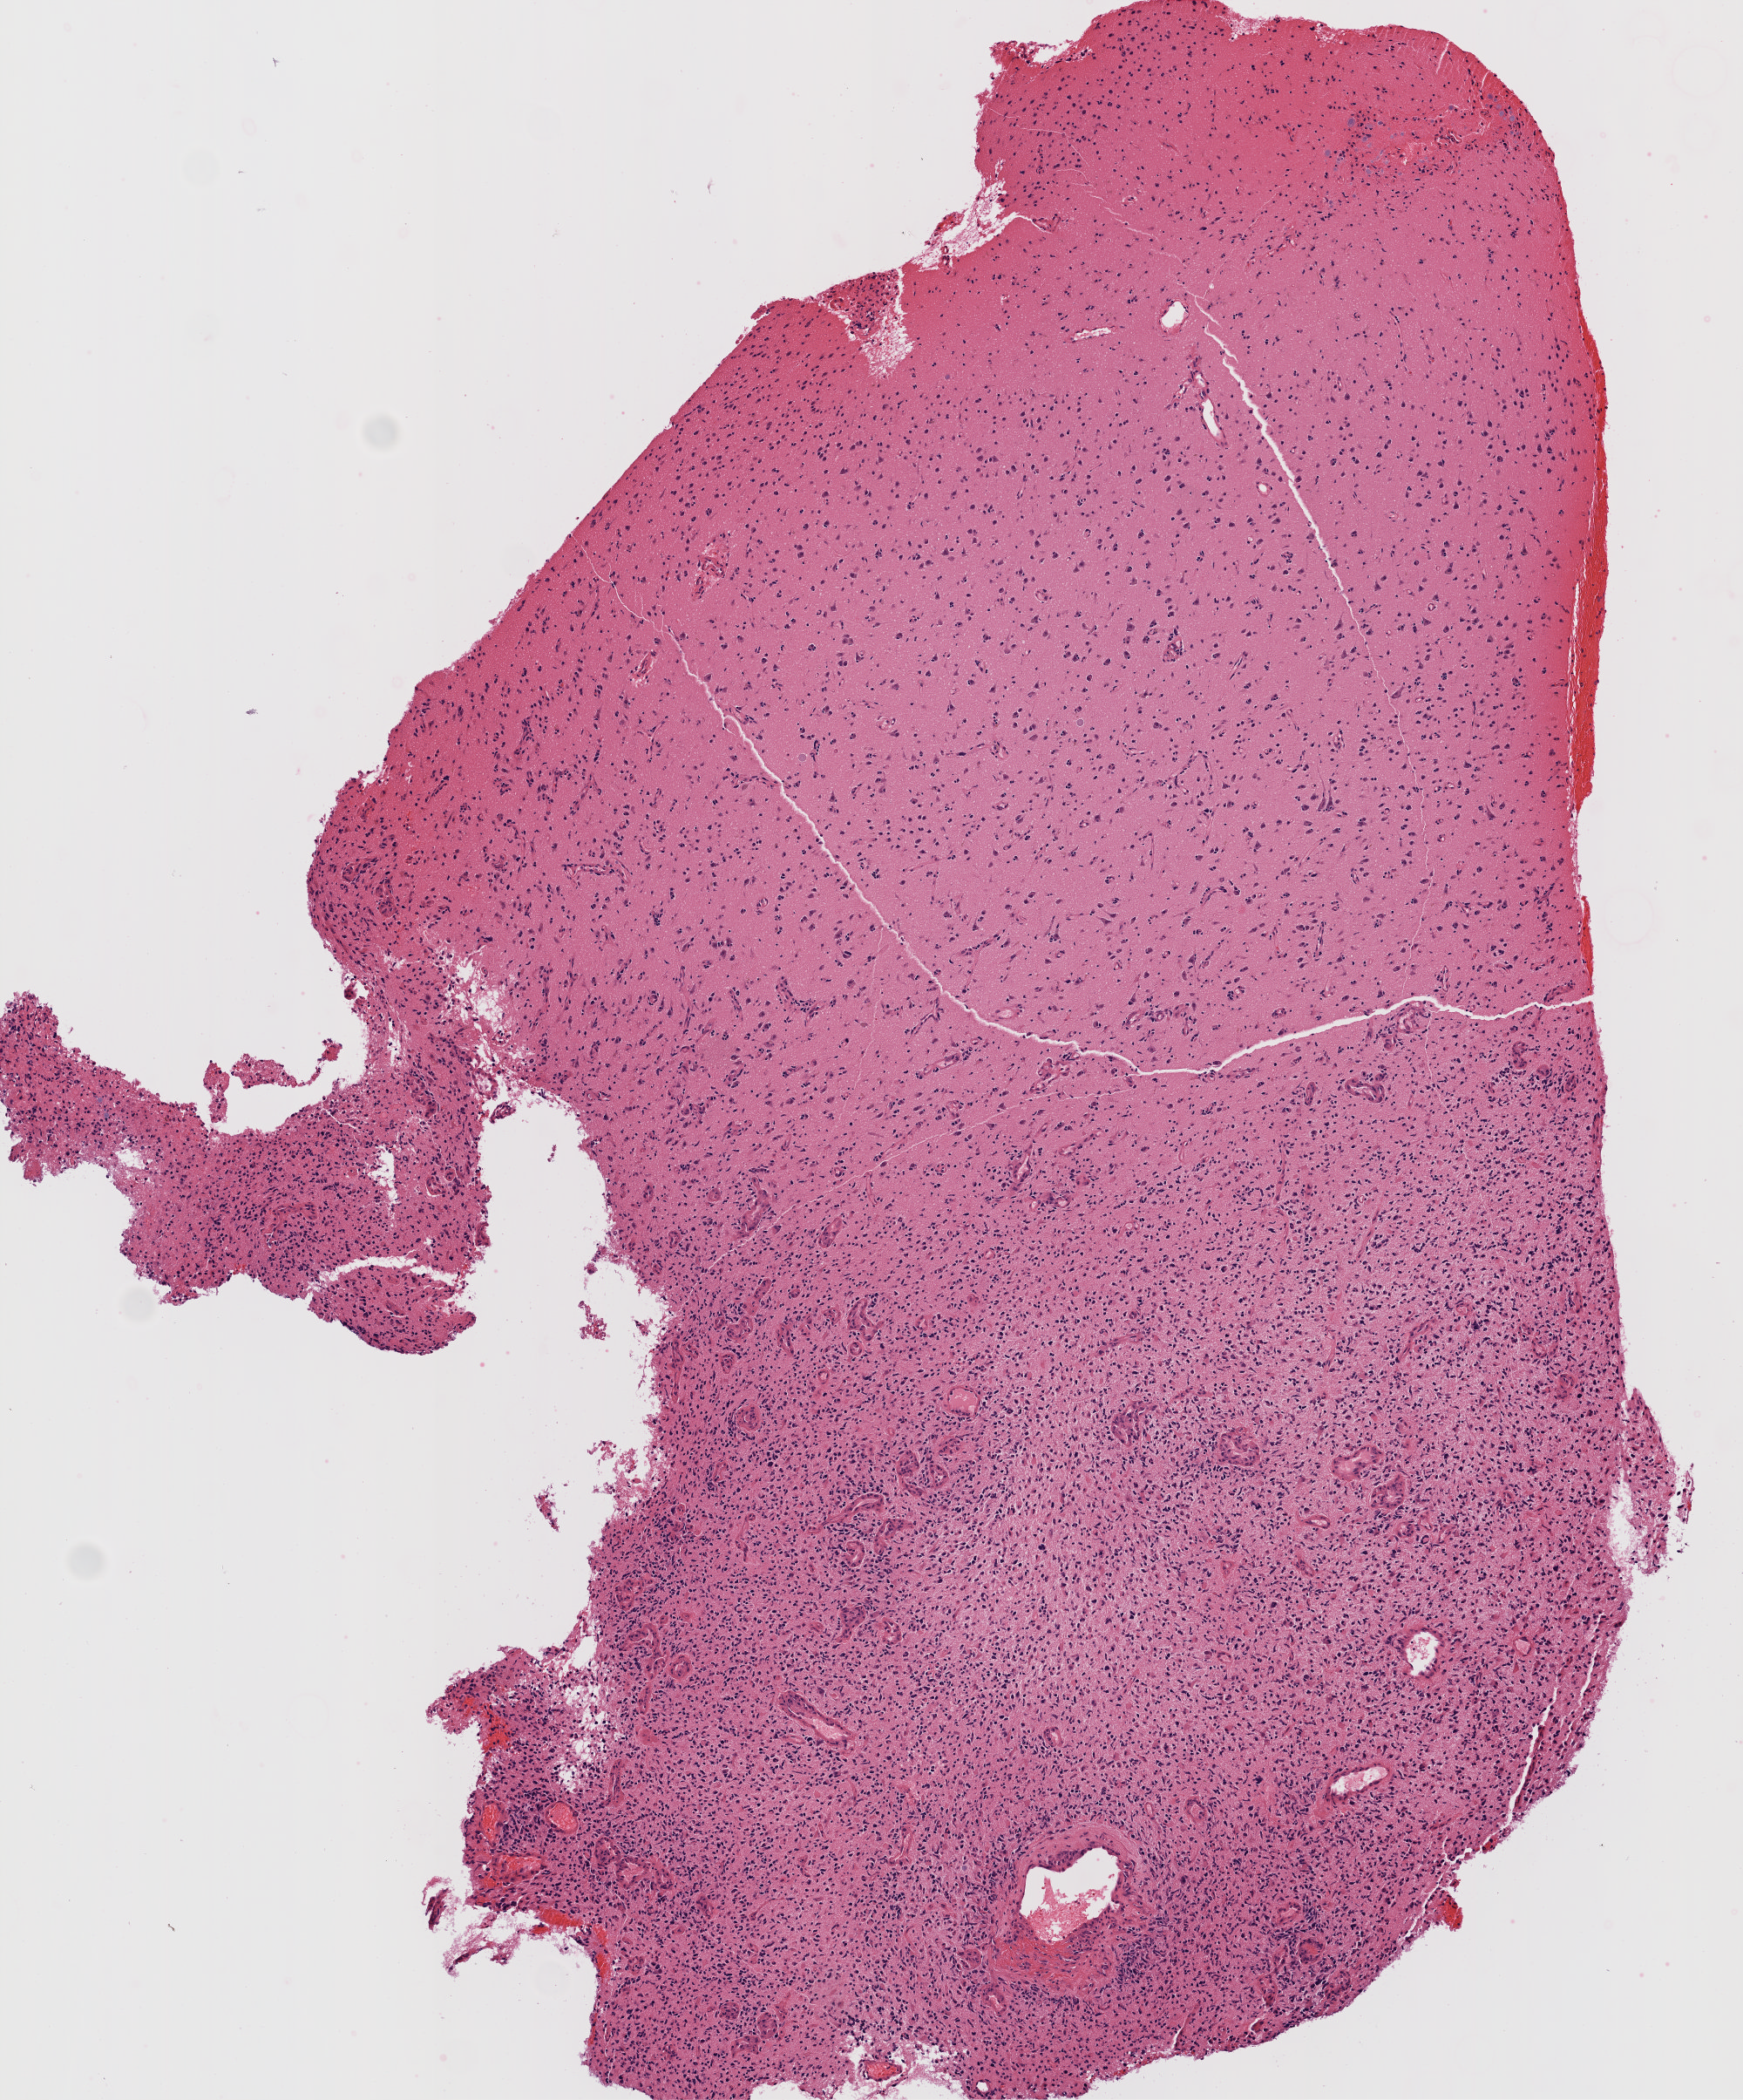
Whole-slide histology image, H&E-stained, a low-resolution overview of the entire scanned area, about 4.0 x 4.8 mm; formalin-fixed paraffin-embedded (FFPE) diagnostic section; sample: primary tumour, brain. Male, age 54 years at initial diagnosis.
- pathologic diagnosis: Glioblastoma